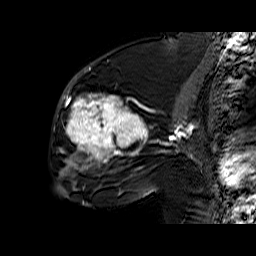
Breast MRI (dynamic contrast-enhanced), one sagittal slice. Position 31 of 60 along the scan axis. Dynamic contrast-enhanced series, time point 2 of 6 at this slice position (early post-contrast). 1.5 T. TE 6.4 ms, TR 32.9 ms. 4 mm slice thickness. 256 × 256 image matrix, field of view 200 × 200 mm. Female patient. From the clinical record (not read from this slice): setting: breast cancer imaged before/during neoadjuvant chemotherapy; receptor status: triple-negative.
Annotated regions visible in this slice (semi-automatic segmentation, software-assisted and operator-edited):
- analysis volume of interest (the breast-tissue region the enhancement analysis was run in; not a lesion): bounding box (x1, y1, x2, y2) in pixels: (56, 65, 158, 174)
- tumour enhancement mask (voxels above the 100 % enhancement threshold inside the analysis volume of interest): (61, 70, 148, 170)